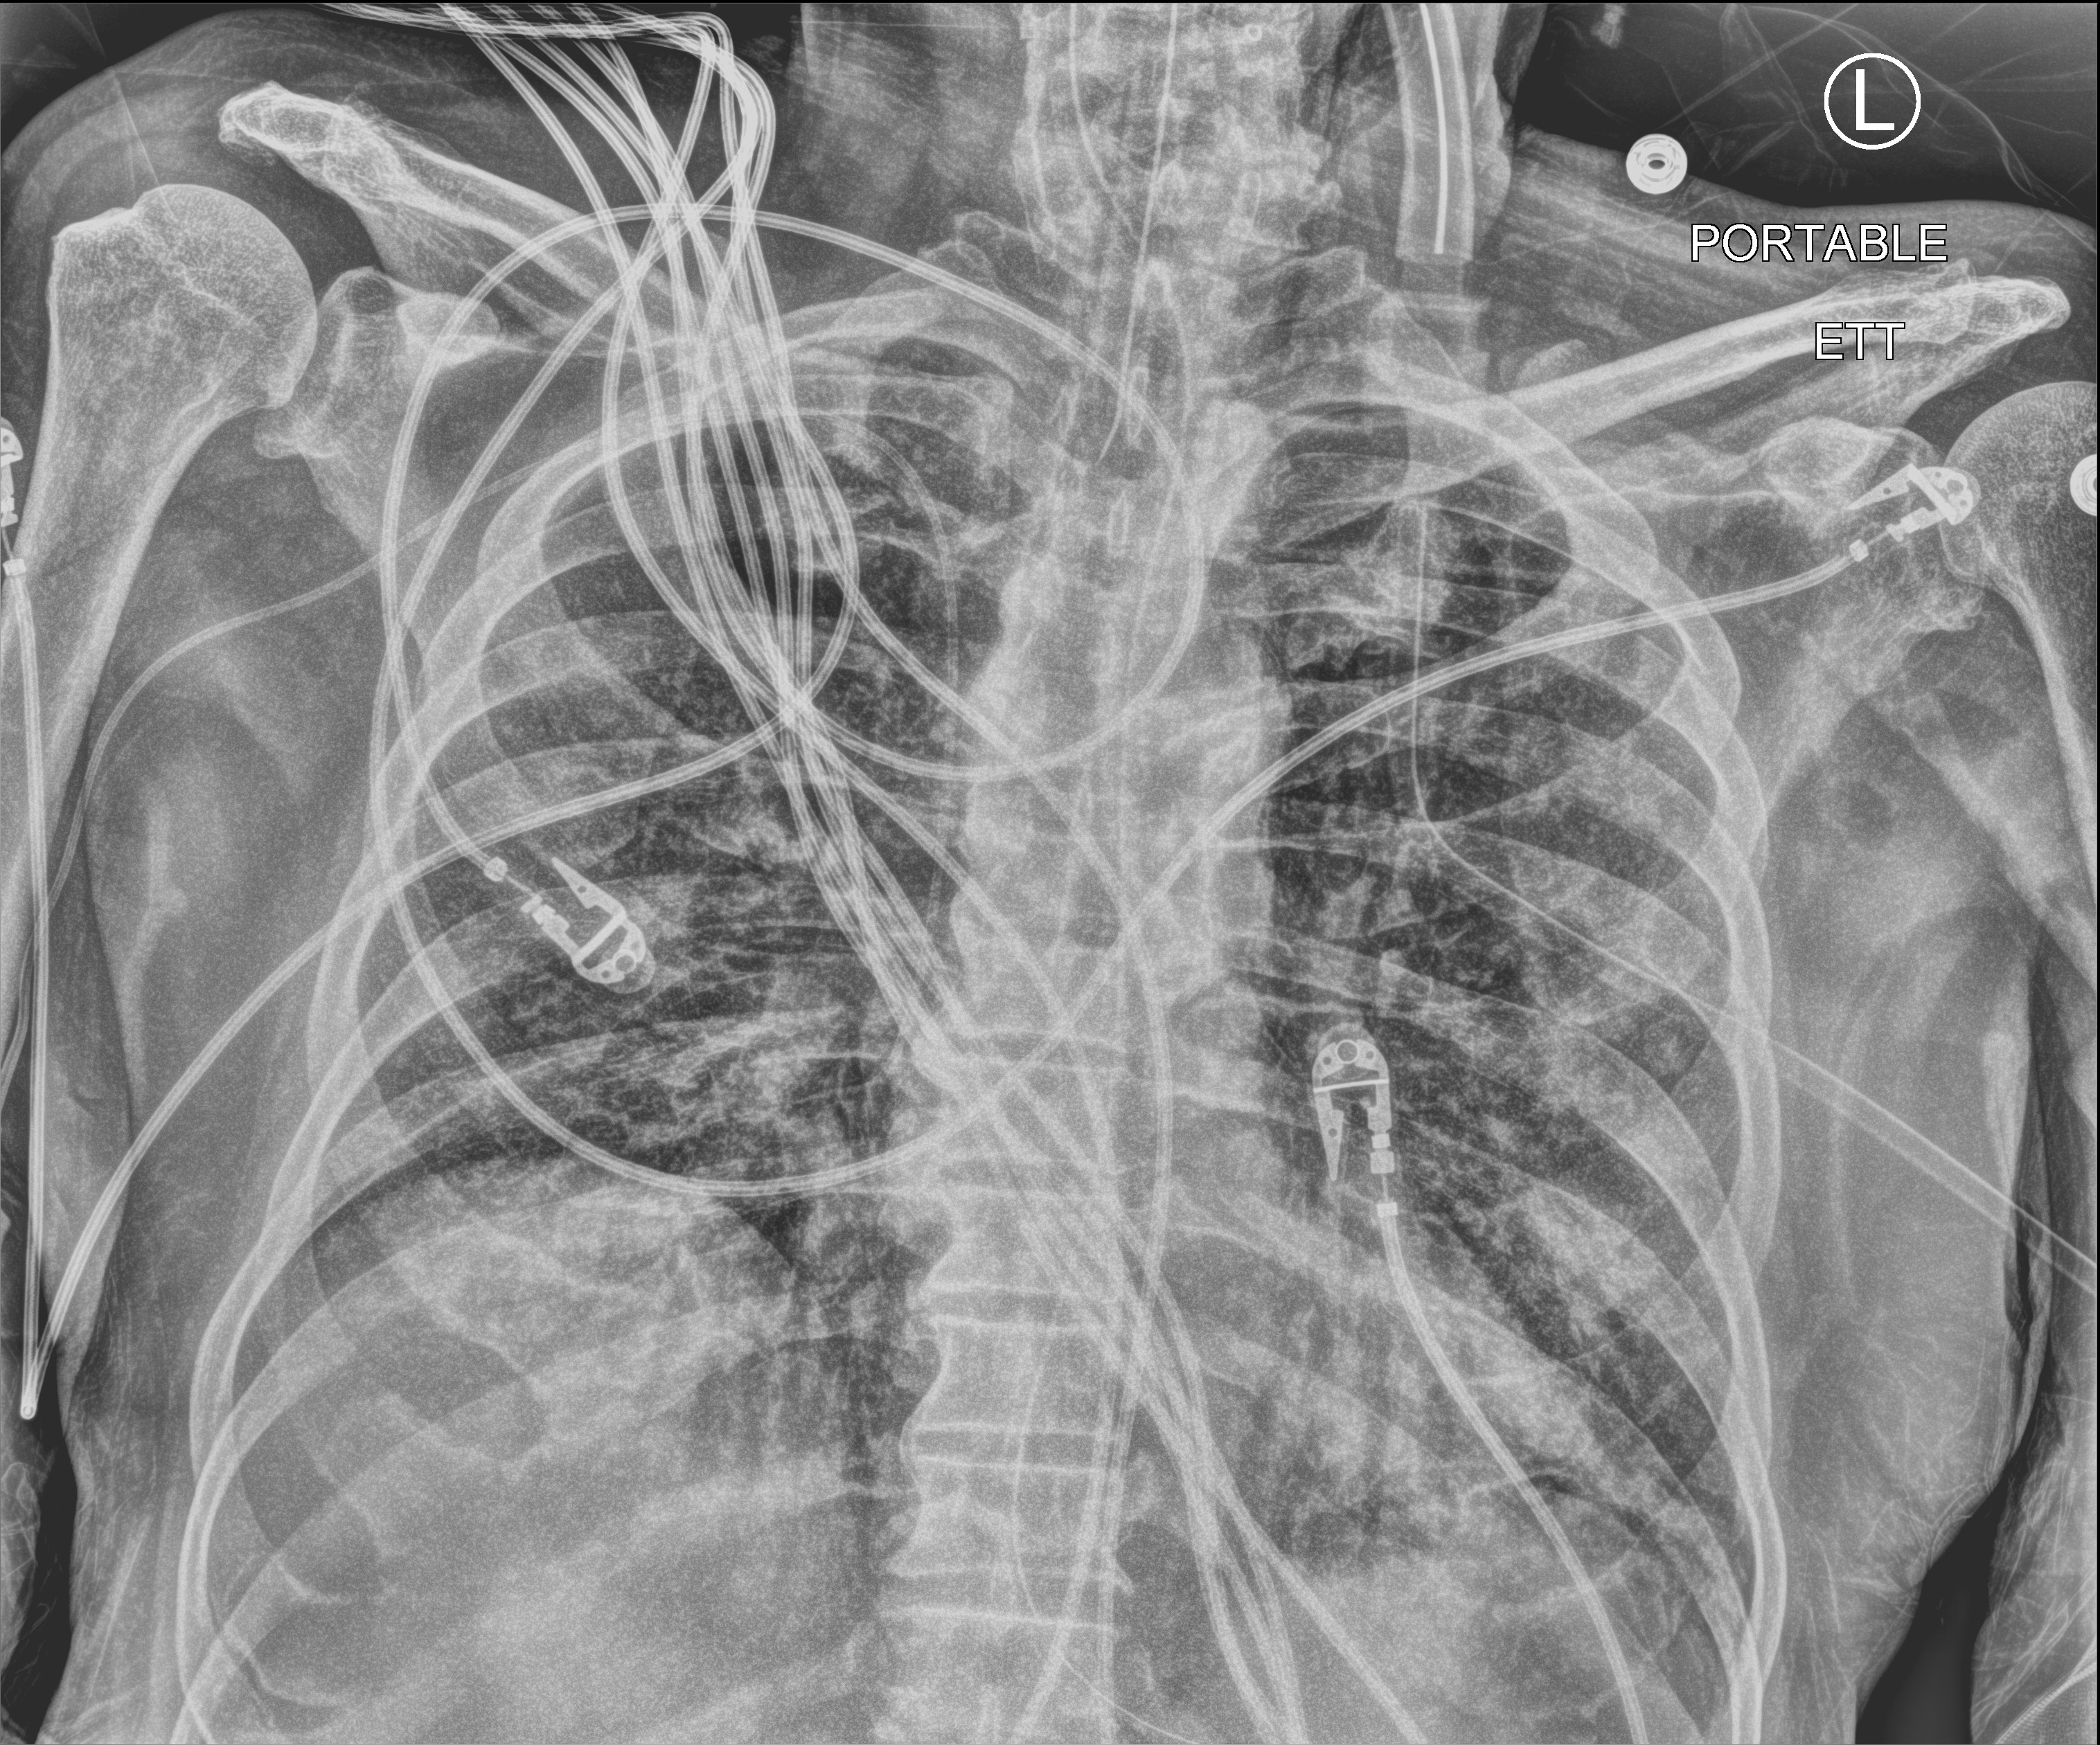
Chest X-ray (portable), anteroposterior (AP) projection. Male patient hospitalised with COVID-19, age 75–90 years.
From the hospital-stay record, not from the radiograph (when in the stay this image was taken is not recorded): mechanically ventilated during this hospital stay: yes.